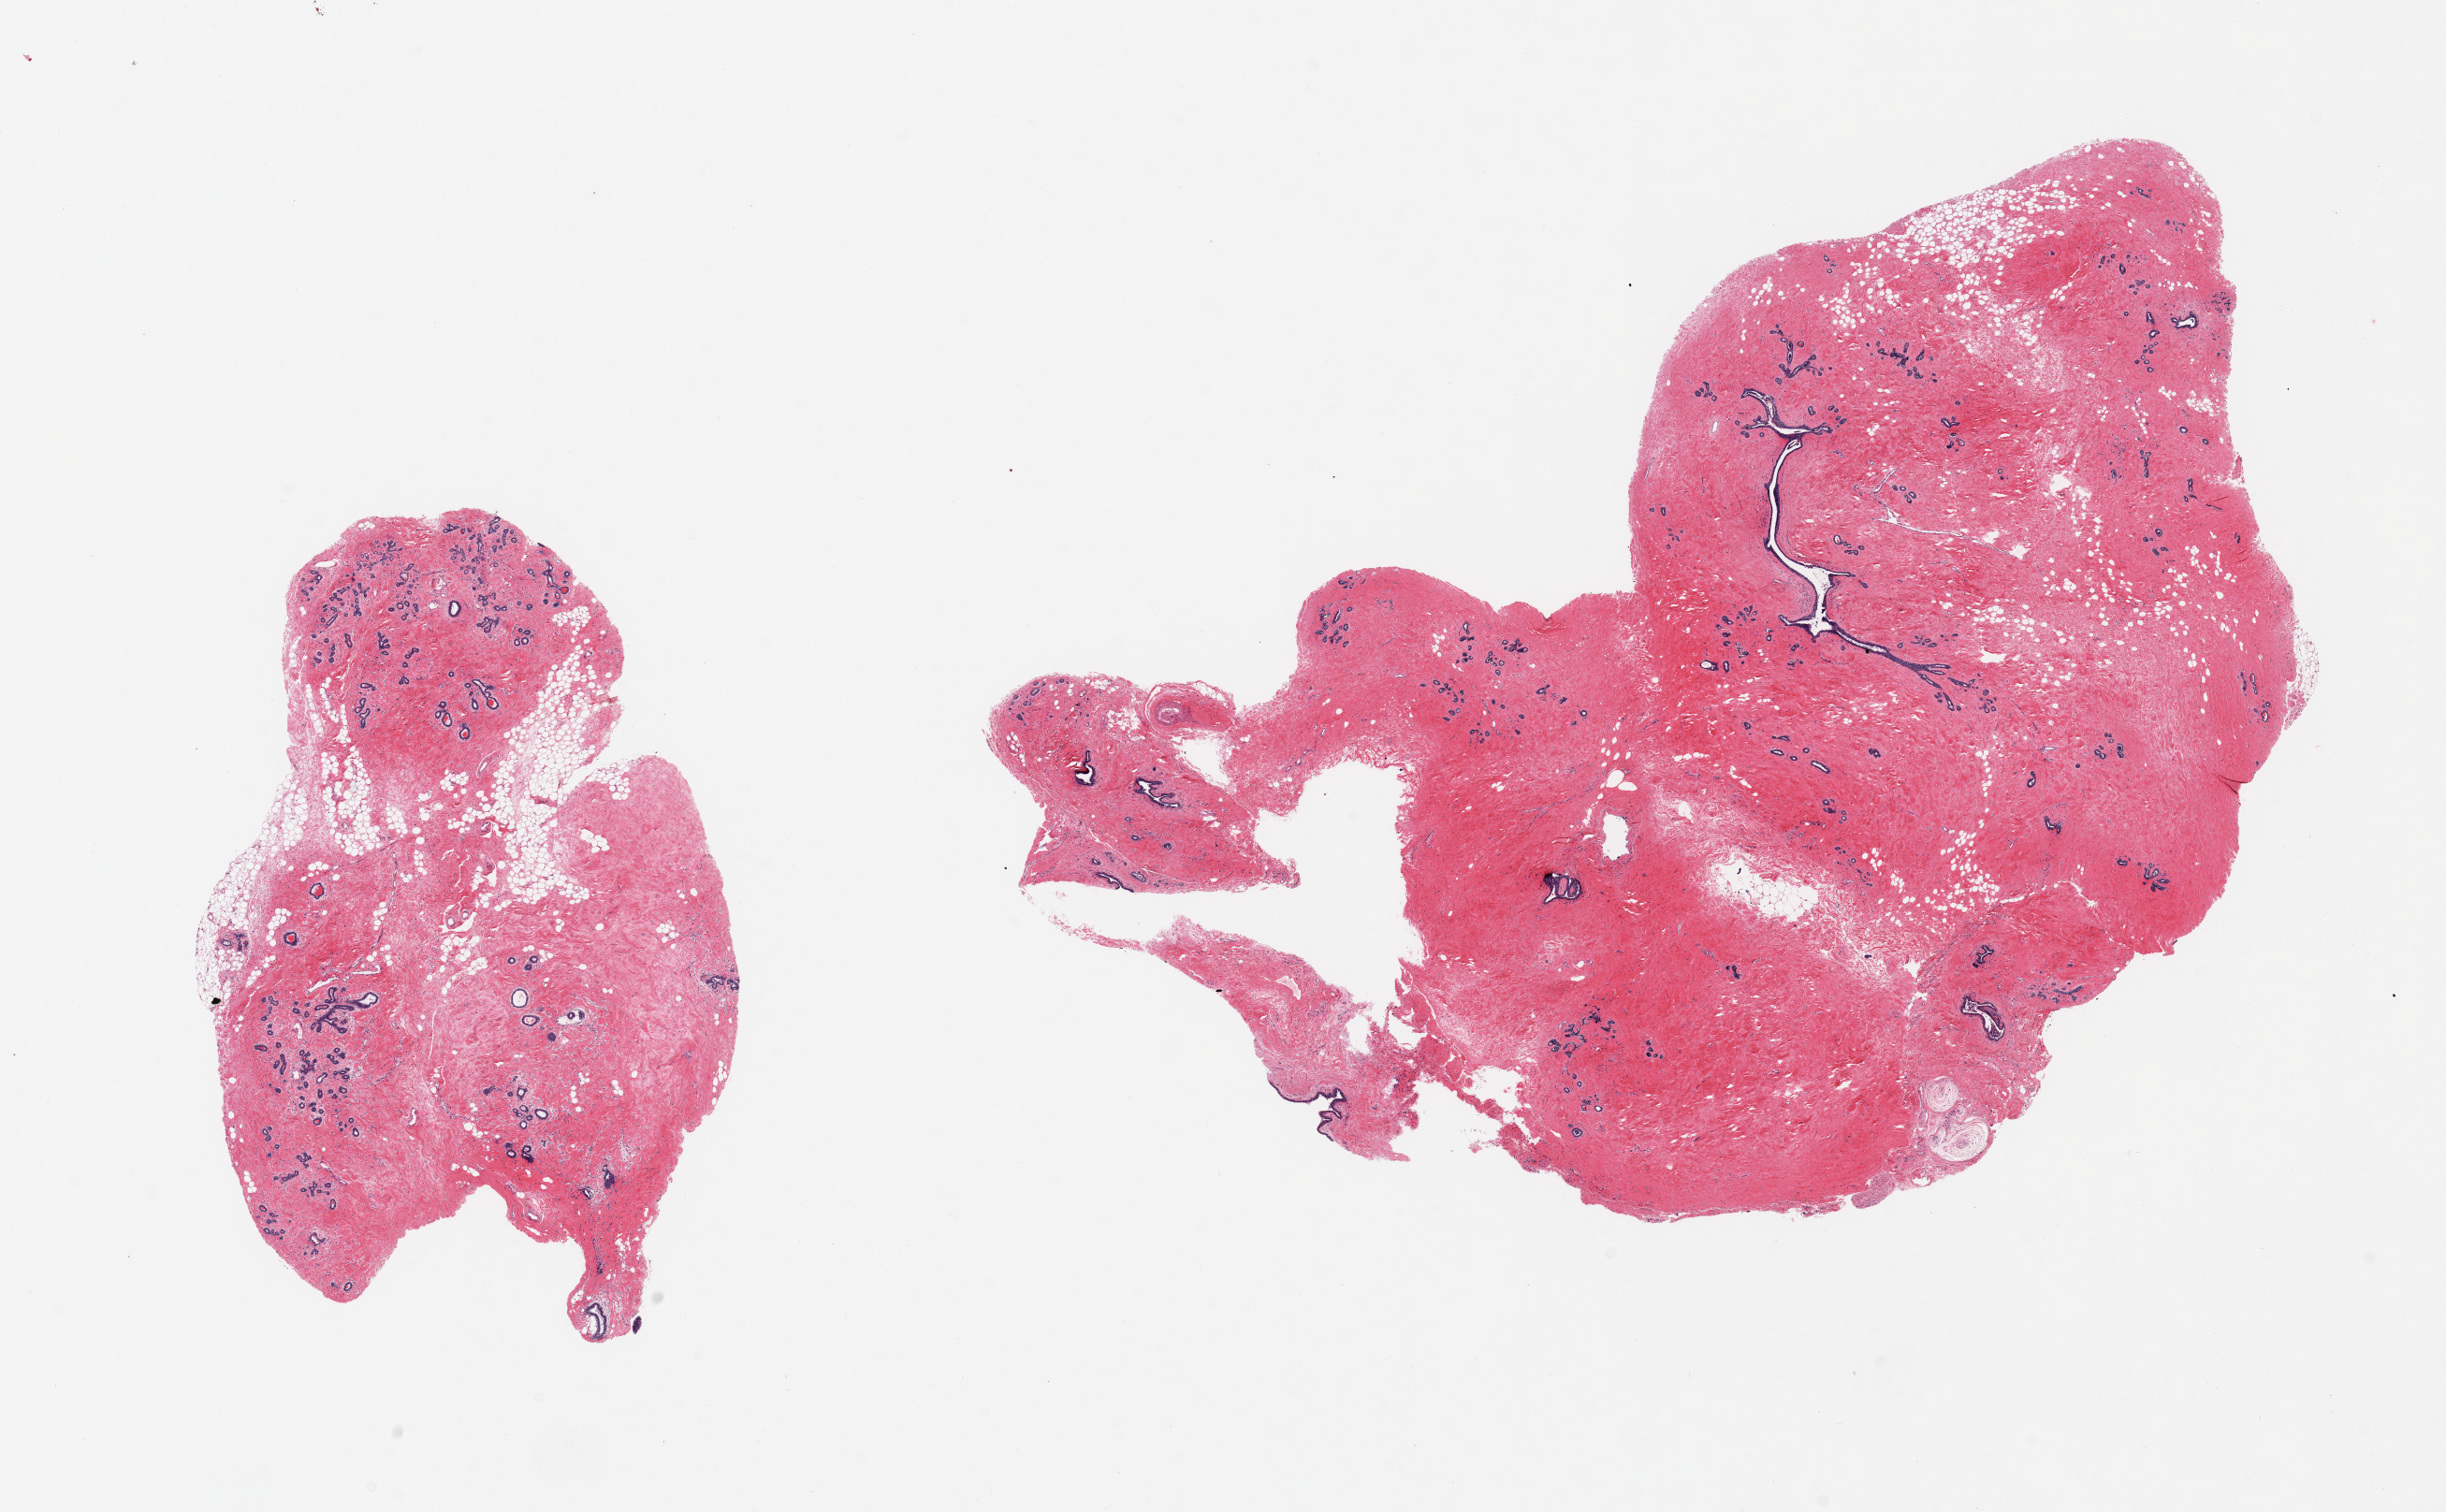
Whole-slide image, H&E stain, brightfield, whole scanned area (about 20.7 x 12.8 mm, acquisition: 20x scan) shown as a low-resolution overview; PAXgene-fixed paraffin-embedded (PFPE) section; section of breast (target tissue); tissue donor sample.
Reviewer comment on this tissue sample: 2 pieces; atrophic ductal and lobular units; dense fibrosis.